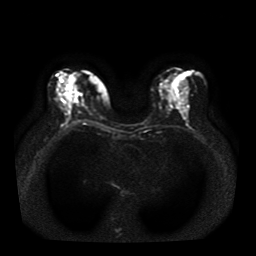
Breast MRI, one axial slice; position 19 of 41 along the scan axis; diffusion-weighted series; image 2 of 4 stored at this slice position (different b-values; order by instance number); 1.5 T; 256 × 256 image matrix. Female patient.
Structures marked on this image (expert manual segmentation):
- tumour on diffusion-weighted imaging: box from (x=67, y=87) to (x=73, y=97) px